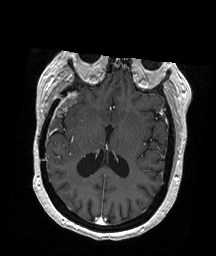
Brain MRI from a brain-tumour surgery series, one axial slice; slice 97 of 192 in the series (ordered by position); T1-weighted post-contrast; 1 mm slice thickness; 216 × 256 image matrix, field of view 211 × 250 mm. From the clinical record (not read from this slice): histopathology: Glioblastoma; WHO grade: 4; IDH mutation: no; tumour location: Right Temporal.
Annotated regions visible in this slice (expert manual segmentation):
- tumour: bounding box (x1, y1, x2, y2) in pixels: (57, 93, 77, 113)